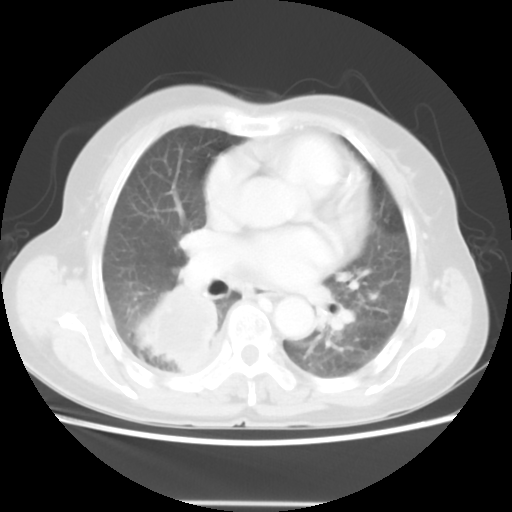
Chest CT, one axial slice. Position 27 of 52 along the scan axis. Reconstruction kernel STANDARD. 140 kVp. Lung window (W 1500 / L -600 HU). 5 mm slice thickness. 512 × 512 image matrix. Patient: female, 67 years. From the clinical record (not read from this slice): clinical TNM (as recorded): T3 N1 M1.
Annotated regions visible in this slice (rectangle marked by the reading radiologist):
- lung tumour (recorded histology: adenocarcinoma): box from (x=138, y=282) to (x=219, y=377) px